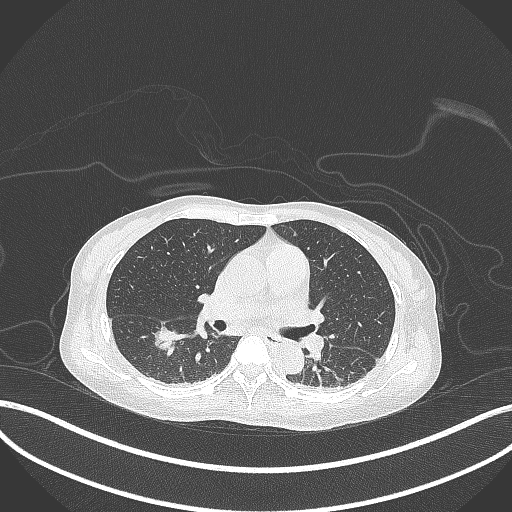
Chest CT, one axial slice. Position 171 of 261 along the scan axis. 120 kVp. Lung window (W 1500 / L -600 HU). 512 × 512 image matrix. Patient: female, 44 years. From the clinical record (not read from this slice): clinical TNM (as recorded): T1c N0 M0.
Structures marked on this image (bounding box drawn by a radiologist):
- lung tumour (recorded histology: adenocarcinoma): bounding box <149,325,180,357> (left, top, right, bottom; pixels)